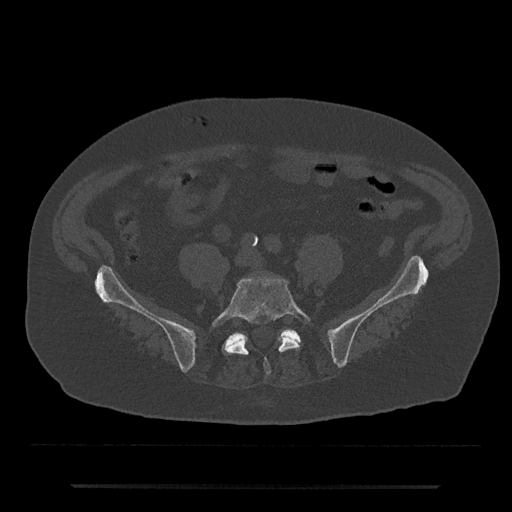
CT including the spine, one axial slice; slice 280 of 797 in the series (ordered by position); bone window (W 1800 / L 400 HU); 0.5 mm slice thickness; 512 × 512 image matrix. Male patient, age 80 years. Case-level facts recorded for this patient, not image findings: primary cancer: prostate; vertebrae with lytic lesions (as recorded): L1, T11.
Structures marked on this image (semi-automatic segmentation, software-assisted and operator-edited):
- L5 vertebra: bounding box (x1, y1, x2, y2) in pixels: (211, 277, 311, 375)